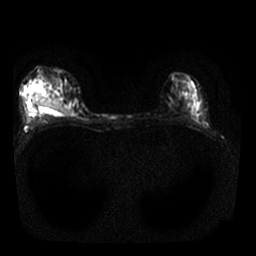
Breast MRI, one axial slice; position 13 of 25 along the scan axis; diffusion-weighted series; image 2 of 4 stored at this slice position (different b-values; order by instance number); 1.5 T; 256 × 256 image matrix, field of view 310 × 310 mm. Female patient.
Structures marked on this image (manually delineated by an expert):
- tumour on diffusion-weighted imaging: bounding box <42,99,71,114> (left, top, right, bottom; pixels)